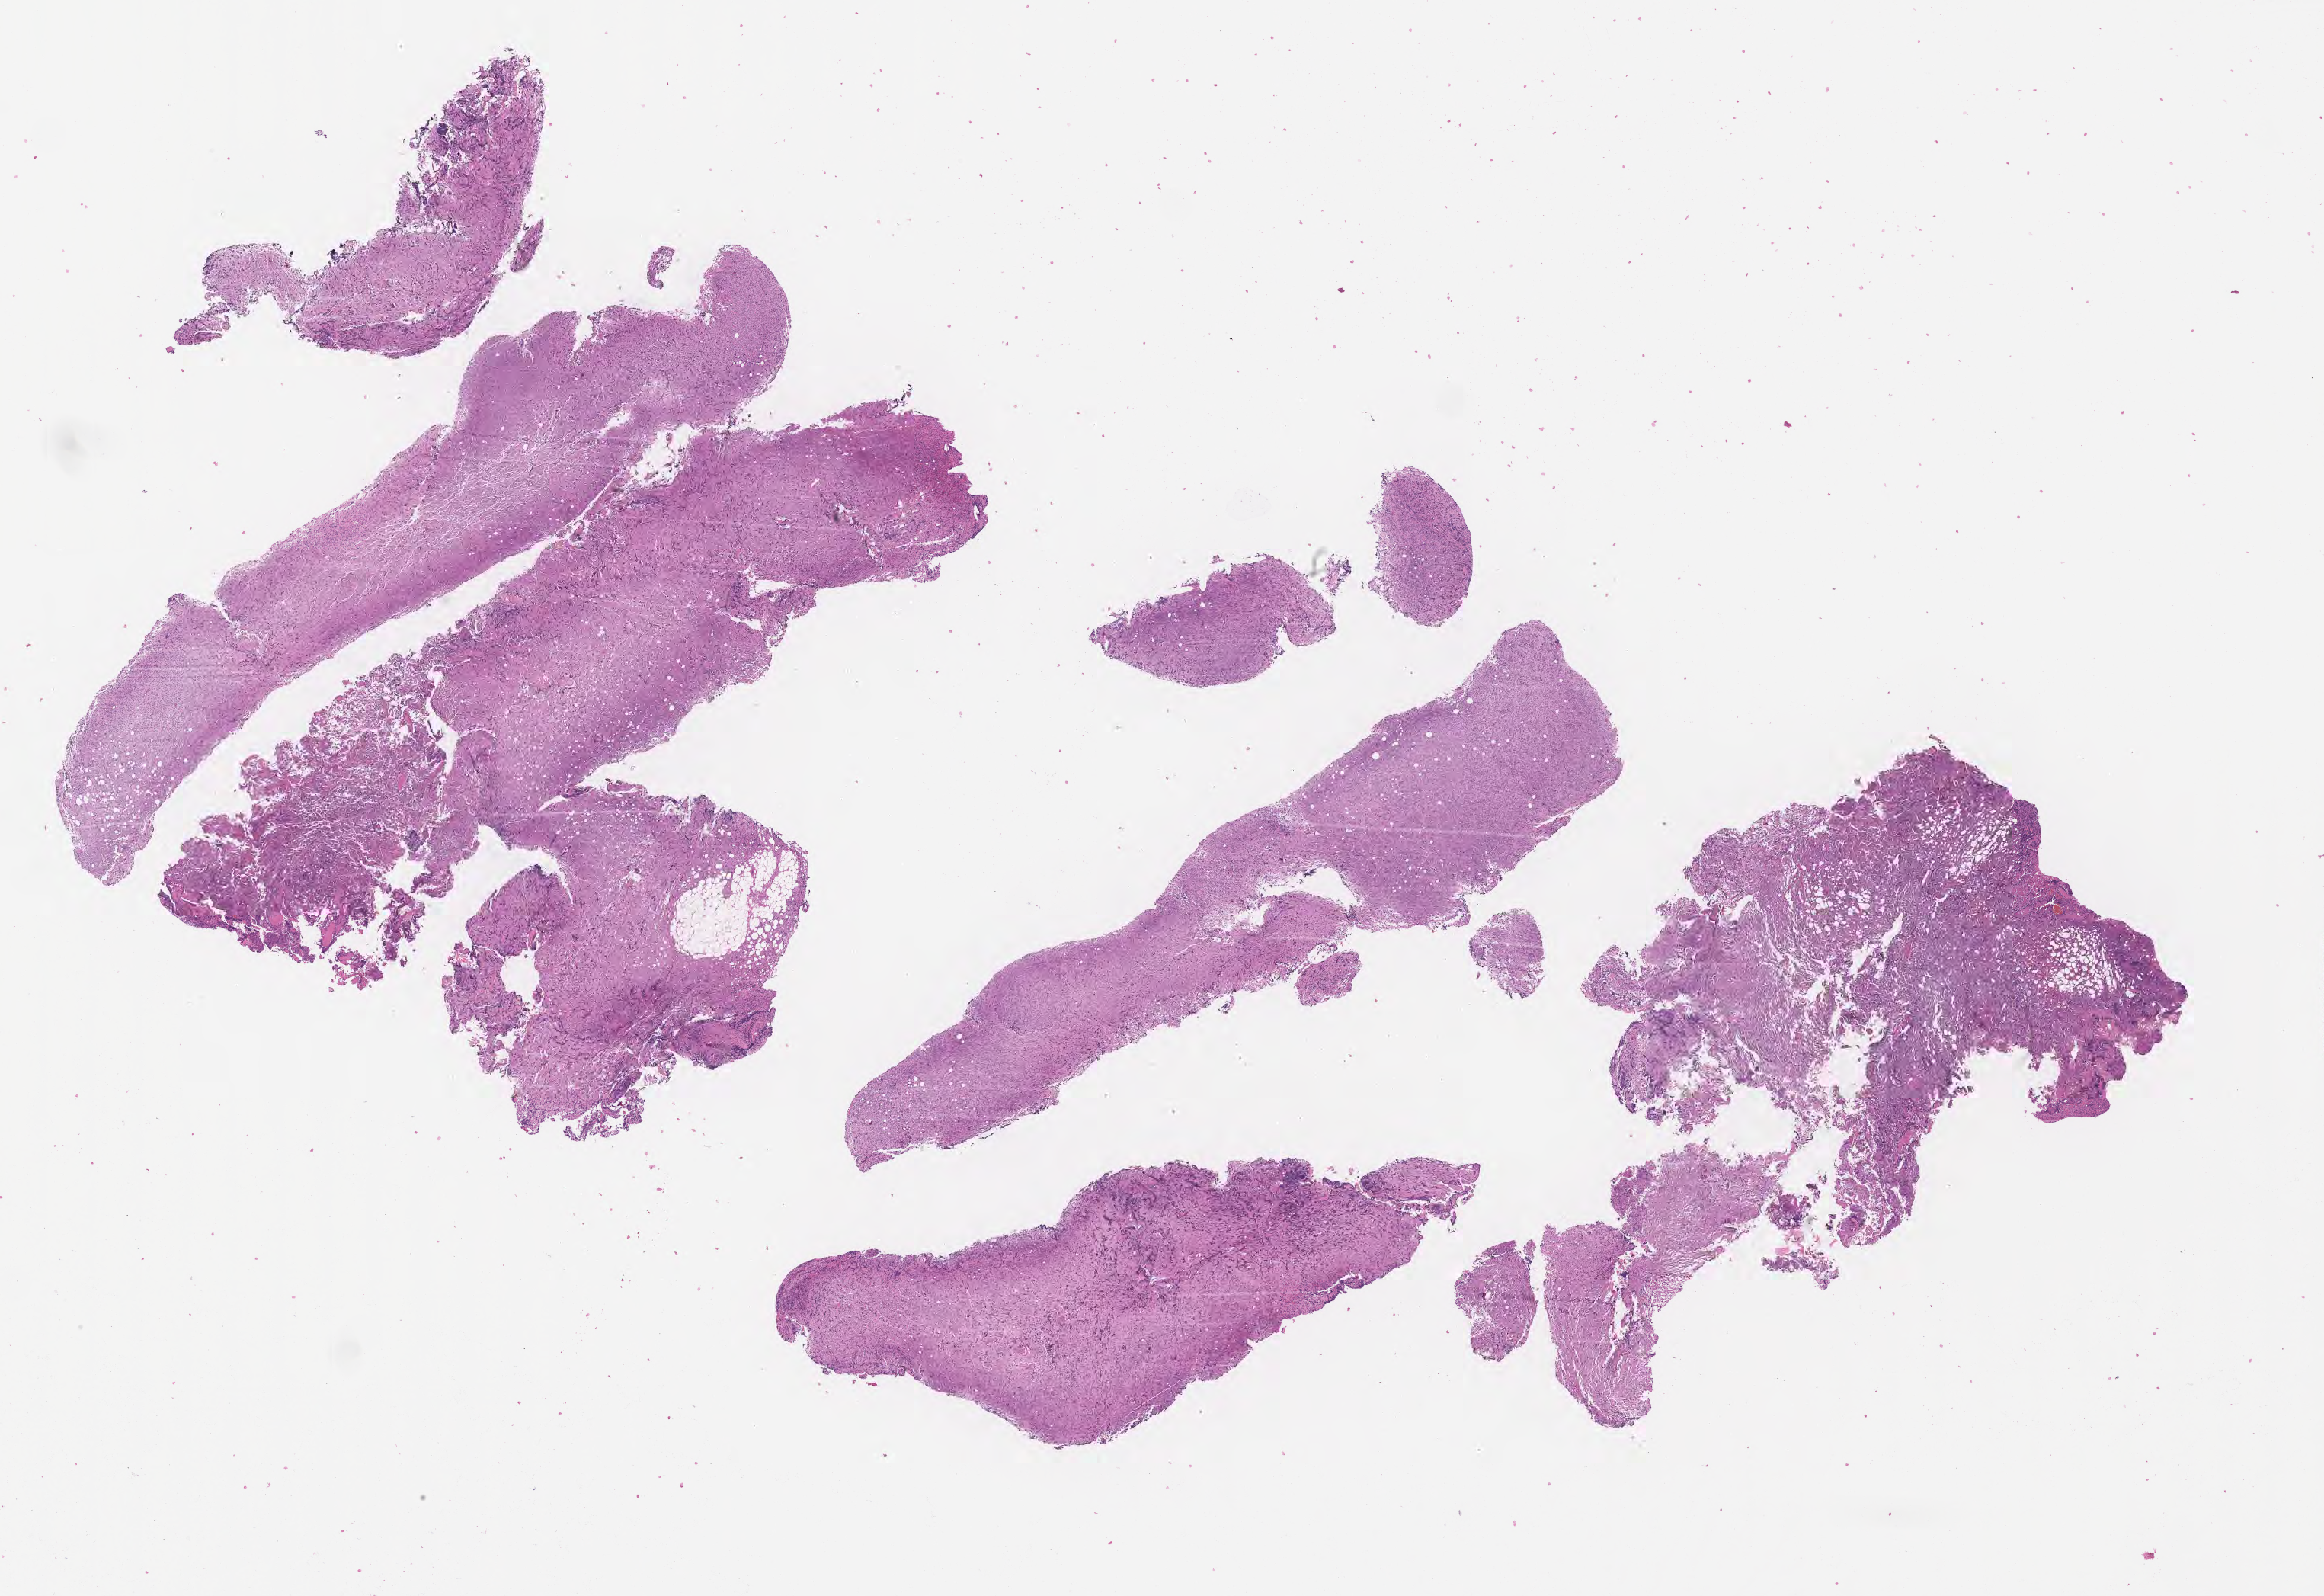
Haematoxylin and eosin whole-slide image, low-resolution overview of the scanned area, about 24.7 x 16.9 mm, specimen: tumor tissue. Patient: male, aged 45.
Histologic diagnosis: Diffuse large B-cell lymphoma, NOS.